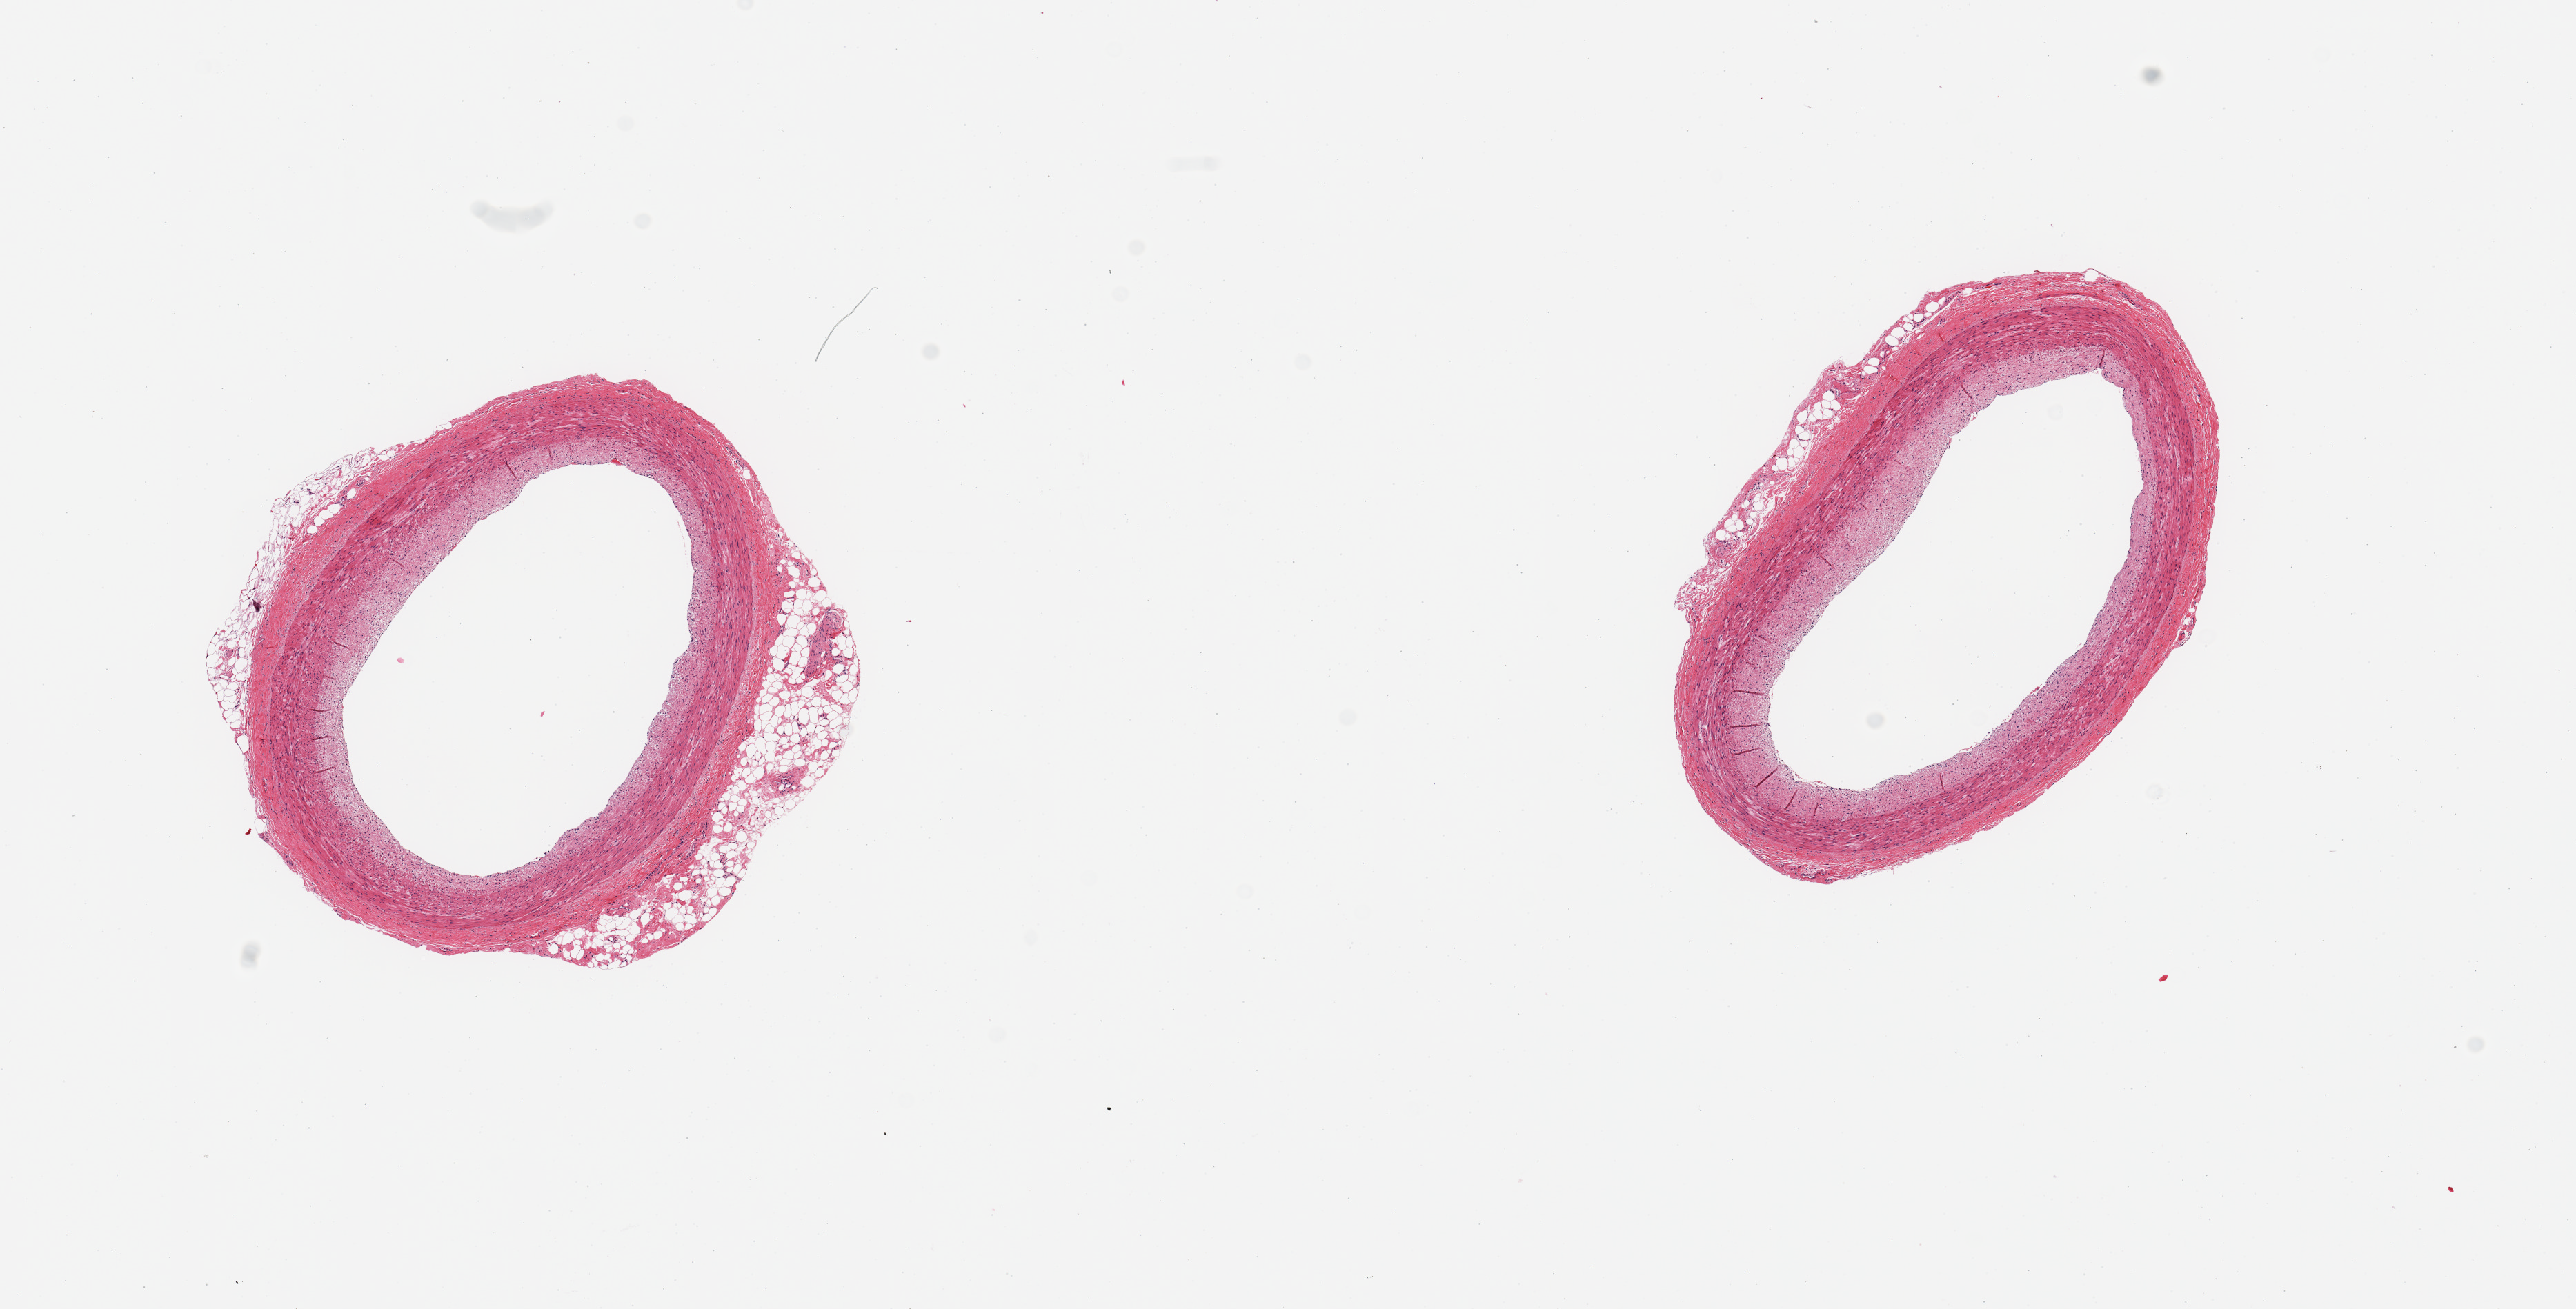
Digitized hematoxylin and eosin (H&E)-stained section — low-resolution overview of the scanned area, about 14.8 x 7.5 mm (from a 20x scan). PAXgene-fixed, paraffin-embedded tissue. Sampled site (target tissue): coronary artery. Donor tissue sample. Donor: male.
Reviewer comment on this tissue sample: 2 pieces, adherent nubbins of fat up to ~0.5mm.